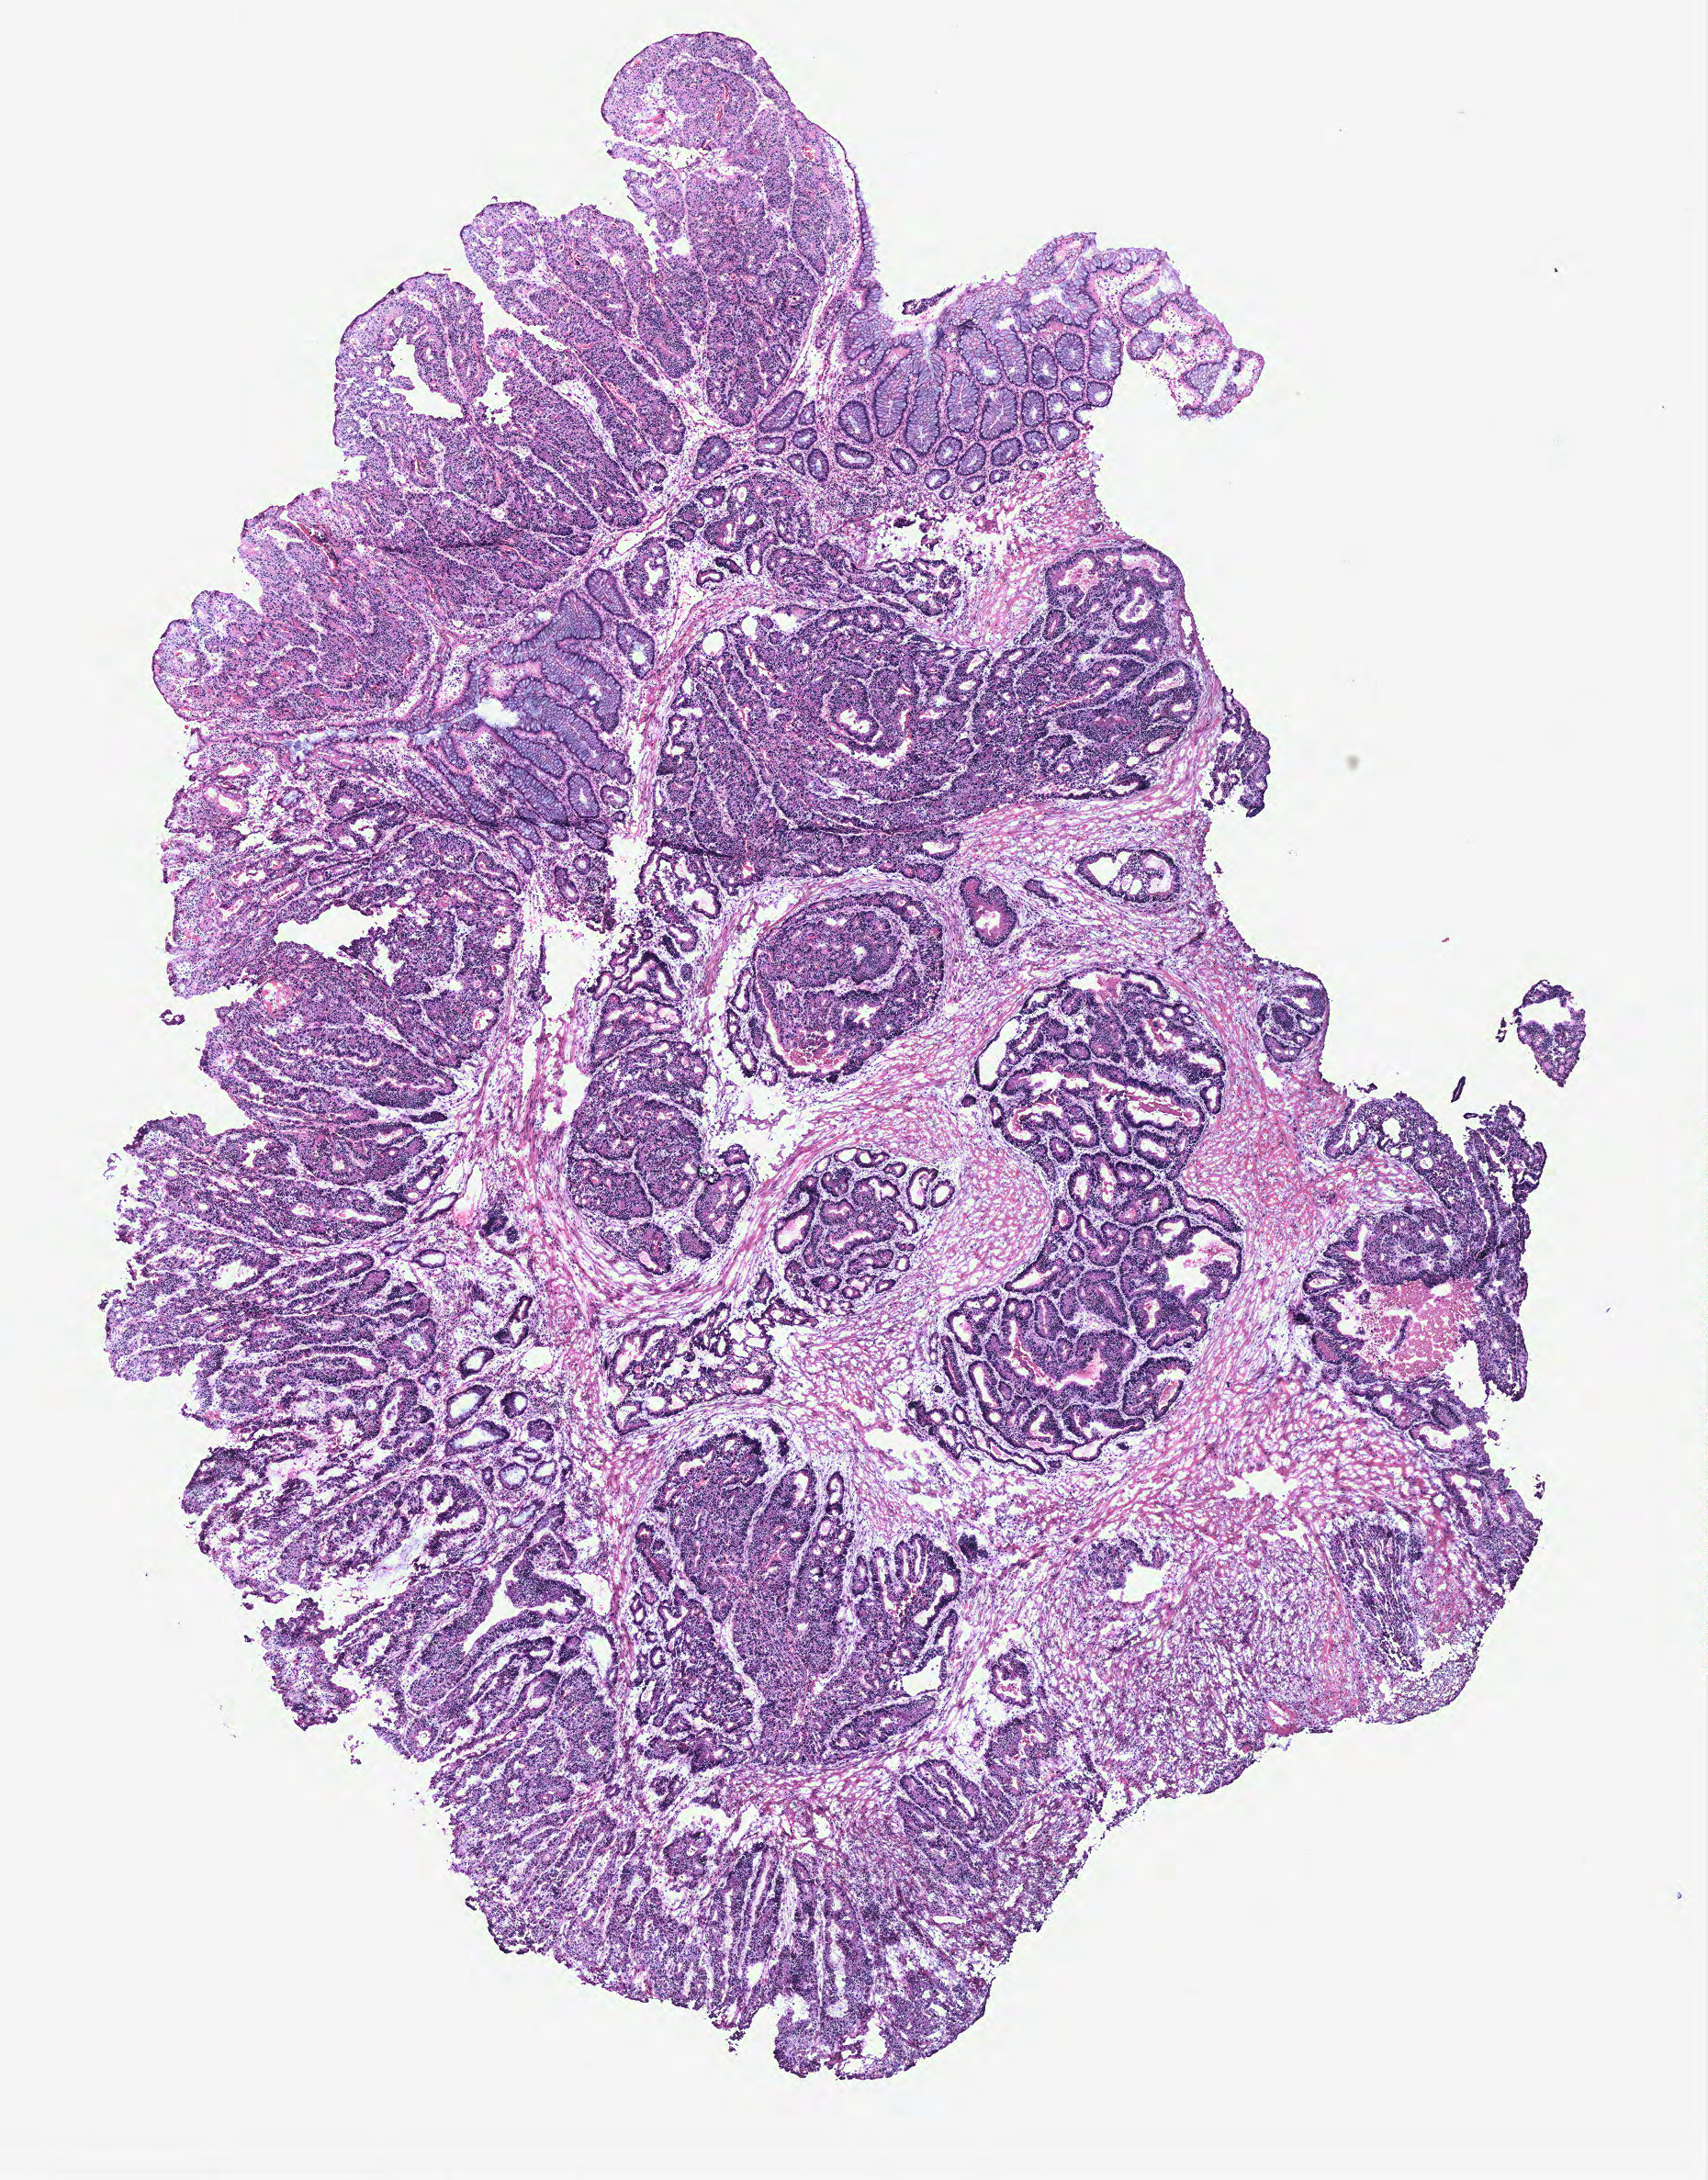
H&E whole-slide image, low-resolution overview of the scanned area, about 7.4 x 9.5 mm; colon, tissue type not recorded.
Patient diagnosis (cohort enrolment): colon cancer (colon).